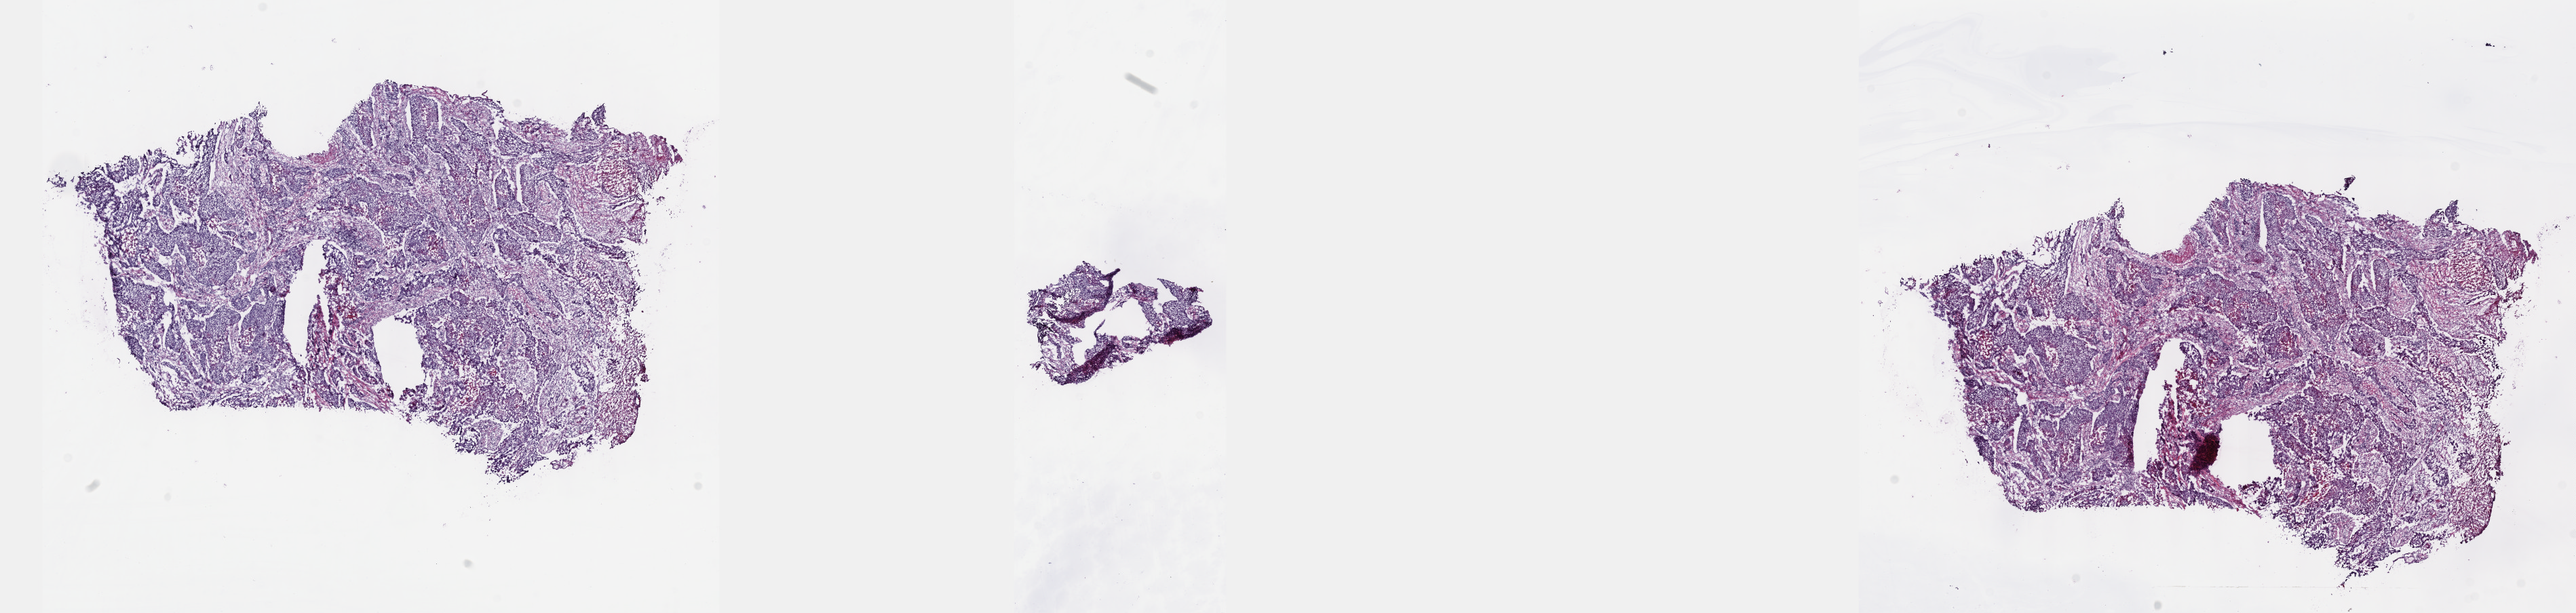
Whole-slide histology image, H&E — a low-resolution overview of the entire scanned area, about 30.7 x 7.3 mm. Frozen section from the top of the tissue portion. Primary tumour sample from the esophagus. Patient: male, age at initial diagnosis 54 years. Histologic grade: GX (grade cannot be assessed). Composition of this section per pathologist review: tumour cells 40%, tumour nuclei 60%, normal cells 0%, stromal cells 52%, necrosis 8%. Infiltration values recorded for this section: lymphocyte infiltration 30%, monocyte infiltration 0%, neutrophil infiltration 3%.
• histologic diagnosis: Squamous cell carcinoma, NOS
• AJCC pathologic stage: III